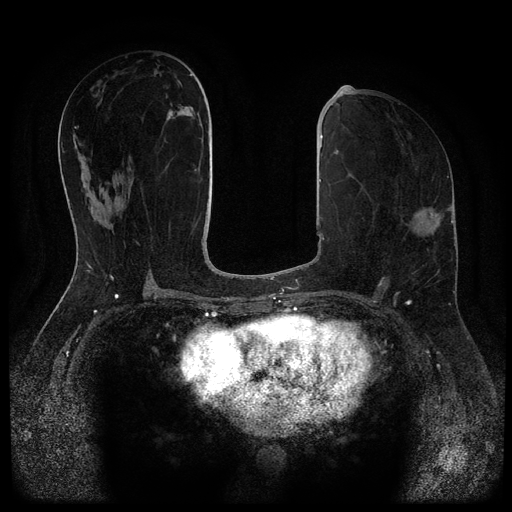
Breast MRI (dynamic contrast-enhanced, multi-phase), one axial slice; position 47 of 116 along the scan axis; dynamic contrast-enhanced series, time point 2 of 5 at this slice position (early post-contrast); 1.5 T; TE 2.7 ms, TR 5.4 ms; 2 mm slice thickness; 512 × 512 image matrix, field of view 330 × 330 mm. Patient: female, 58 years.
Outlined on this slice (semi-automatically segmented with operator editing):
- breast lesion (labelled benign in the annotation): bounding box [x1, y1, x2, y2] px = [167, 103, 202, 126]